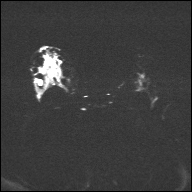
Breast MRI, one axial slice. Position 21 of 32 along the scan axis. Diffusion-weighted series; image 2 of 4 stored at this slice position (different b-values; order by instance number). 1.5 T. 4 mm slice thickness. 192 × 192 image matrix, field of view 360 × 360 mm. Female patient.
Outlined on this slice (manually delineated by an expert):
- tumour on diffusion-weighted imaging: box from (x=46, y=61) to (x=52, y=69) px